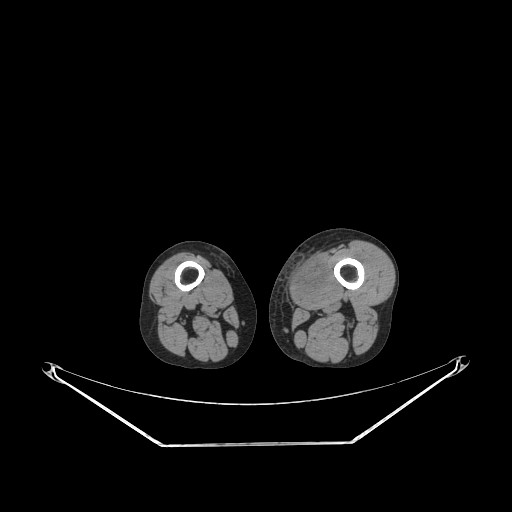
CT of an extremity soft-tissue mass (from a PET/CT study), one axial slice. Slice 209 of 267 in the series (ordered by position). 140 kVp. Soft-tissue window (W 400 / L 40 HU). 3.75 mm slice thickness. 512 × 512 image matrix, field of view 500 × 500 mm. Male patient. Case-level facts recorded for this patient, not image findings: histological type: pleiomorphic leiomyosarcoma; grade: high; site of the primary tumour: left thigh.
Outlined on this slice (expert contour drawn on MRI and transferred to this co-registered scan by the dataset authors):
- gross tumour volume including surrounding oedema: bounding box <290,253,328,303> (left, top, right, bottom; pixels)
- gross tumour volume (mass): <294,258,323,289>